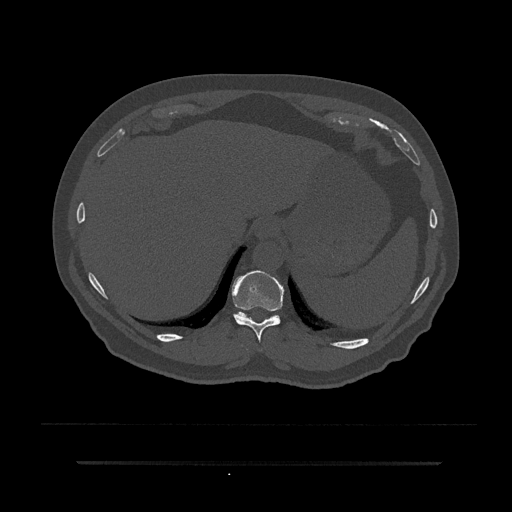
CT including the spine, one axial slice; position 315 of 797 along the scan axis; bone window (W 1800 / L 400 HU); 512 × 512 image matrix, field of view 464 × 464 mm. Patient: male, 59 years. From the clinical record (not read from this slice): primary cancer: bile ducts.
Structures marked on this image (semi-automatically segmented with operator editing):
- T10 vertebra: box from (x=232, y=271) to (x=284, y=341) px
- T11 vertebra: (x=235, y=312)–(x=279, y=320)